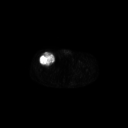
FDG PET of an extremity soft-tissue mass (from a PET/CT study), one axial slice. Position 293 of 311 along the scan axis. 3.27 mm slice thickness. 128 × 128 image matrix, field of view 700 × 700 mm. Male patient, age 56 years. From the clinical record (not read from this slice): histological type: pleiomorphic leiomyosarcoma; grade: intermediate; site of the primary tumour: right thigh.
Structures marked on this image (expert contour drawn on MRI and transferred to this co-registered scan by the dataset authors):
- gross tumour volume including surrounding oedema: box from (x=39, y=52) to (x=55, y=66) px
- gross tumour volume (mass): (x=39, y=52)–(x=55, y=66)